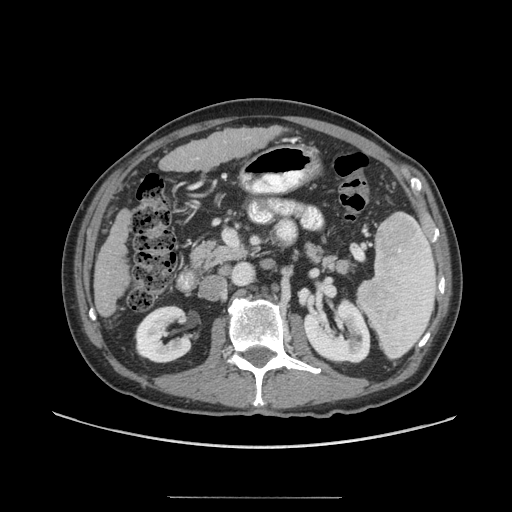
Contrast-enhanced abdominal CT (liver protocol), one axial slice. Position 17 of 71 along the scan axis. 140 kVp. Soft-tissue window (W 400 / L 40 HU). 2.5 mm slice thickness. 512 × 512 image matrix. From the clinical record (not read from this slice): diagnosis: hepatocellular carcinoma (patient treated with transarterial chemoembolisation; whether this scan precedes or follows treatment is not stated here); TNM stage (as recorded): Stage-I; Child-Pugh class: A; tumour differentiation: well differentiated; tumour nodularity: uninodular.
Outlined on this slice (semi-automatically segmented with operator editing):
- liver parenchyma outside the tumour (the mass and vessels are separate outlines, so this box may not span the whole liver): bounding box [x1, y1, x2, y2] px = [94, 126, 282, 318]